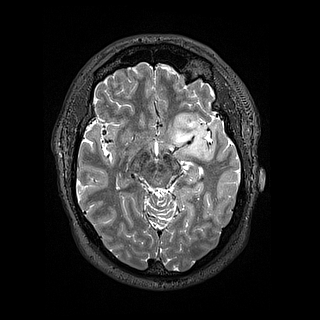
Brain MRI from a brain-tumour surgery series, one axial slice; position 93 of 144 along the scan axis; 1.2 mm slice thickness; 320 × 320 image matrix, field of view 254 × 254 mm. From the clinical record (not read from this slice): histopathology: Astrocytoma; WHO grade: 2; IDH mutation: yes; tumour location: Left Insular.
Structures marked on this image (expert manual segmentation):
- tumour: bounding box [x1, y1, x2, y2] px = [172, 110, 209, 158]